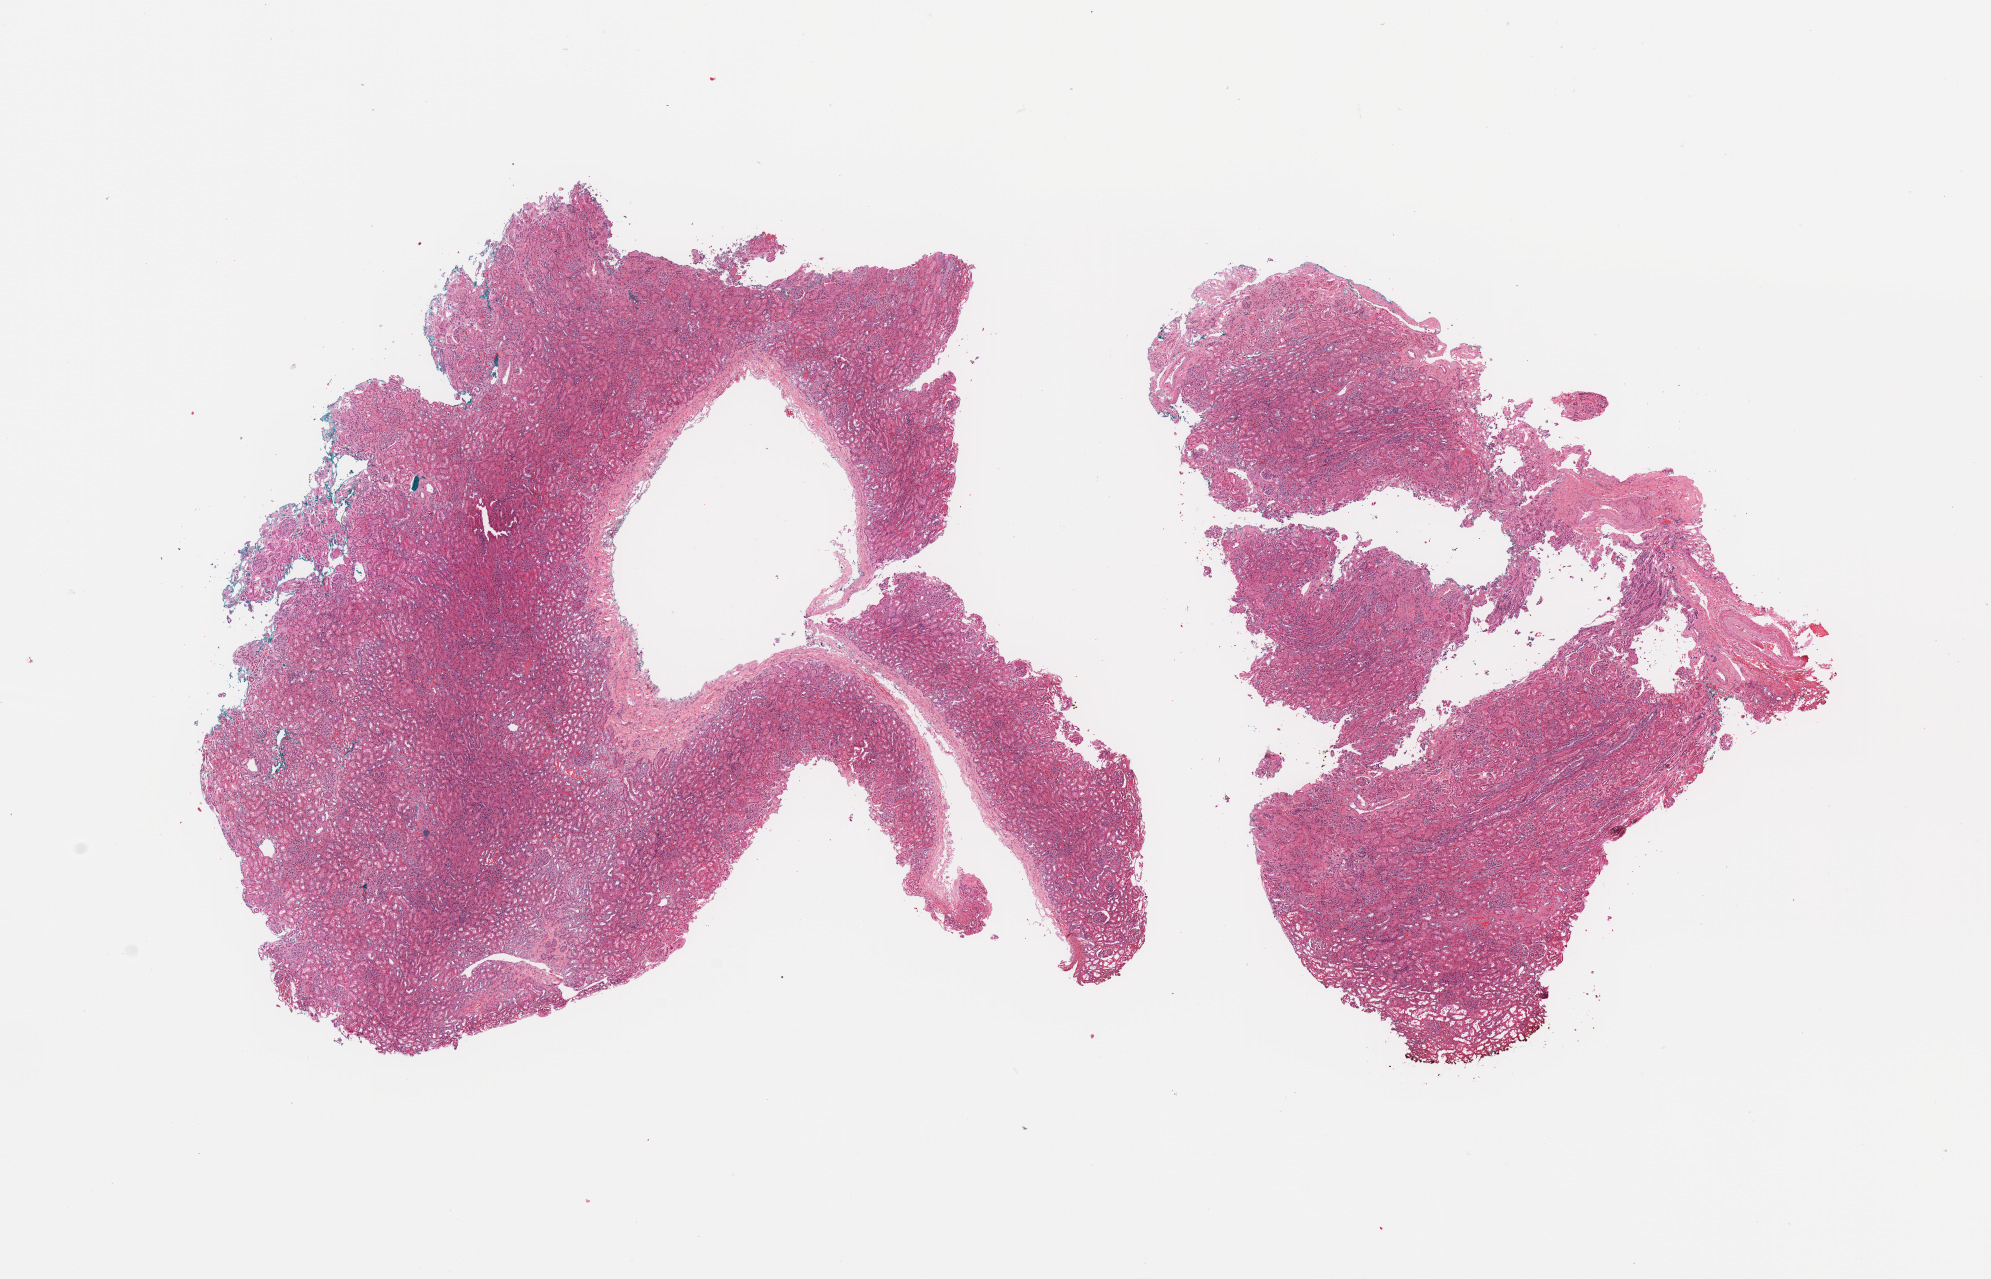
Digitized H&E-stained tissue section (whole slide) — shown as a low-resolution overview of the whole scanned area (about 15.8 x 10.1 mm, slide scanned at 20x), normal (non-tumour) tissue sample, sampled site: kidney. 63-year-old male patient.
* this section: normal (non-tumour) tissue from the same patient
* patient diagnosis: Renal cell carcinoma, NOS